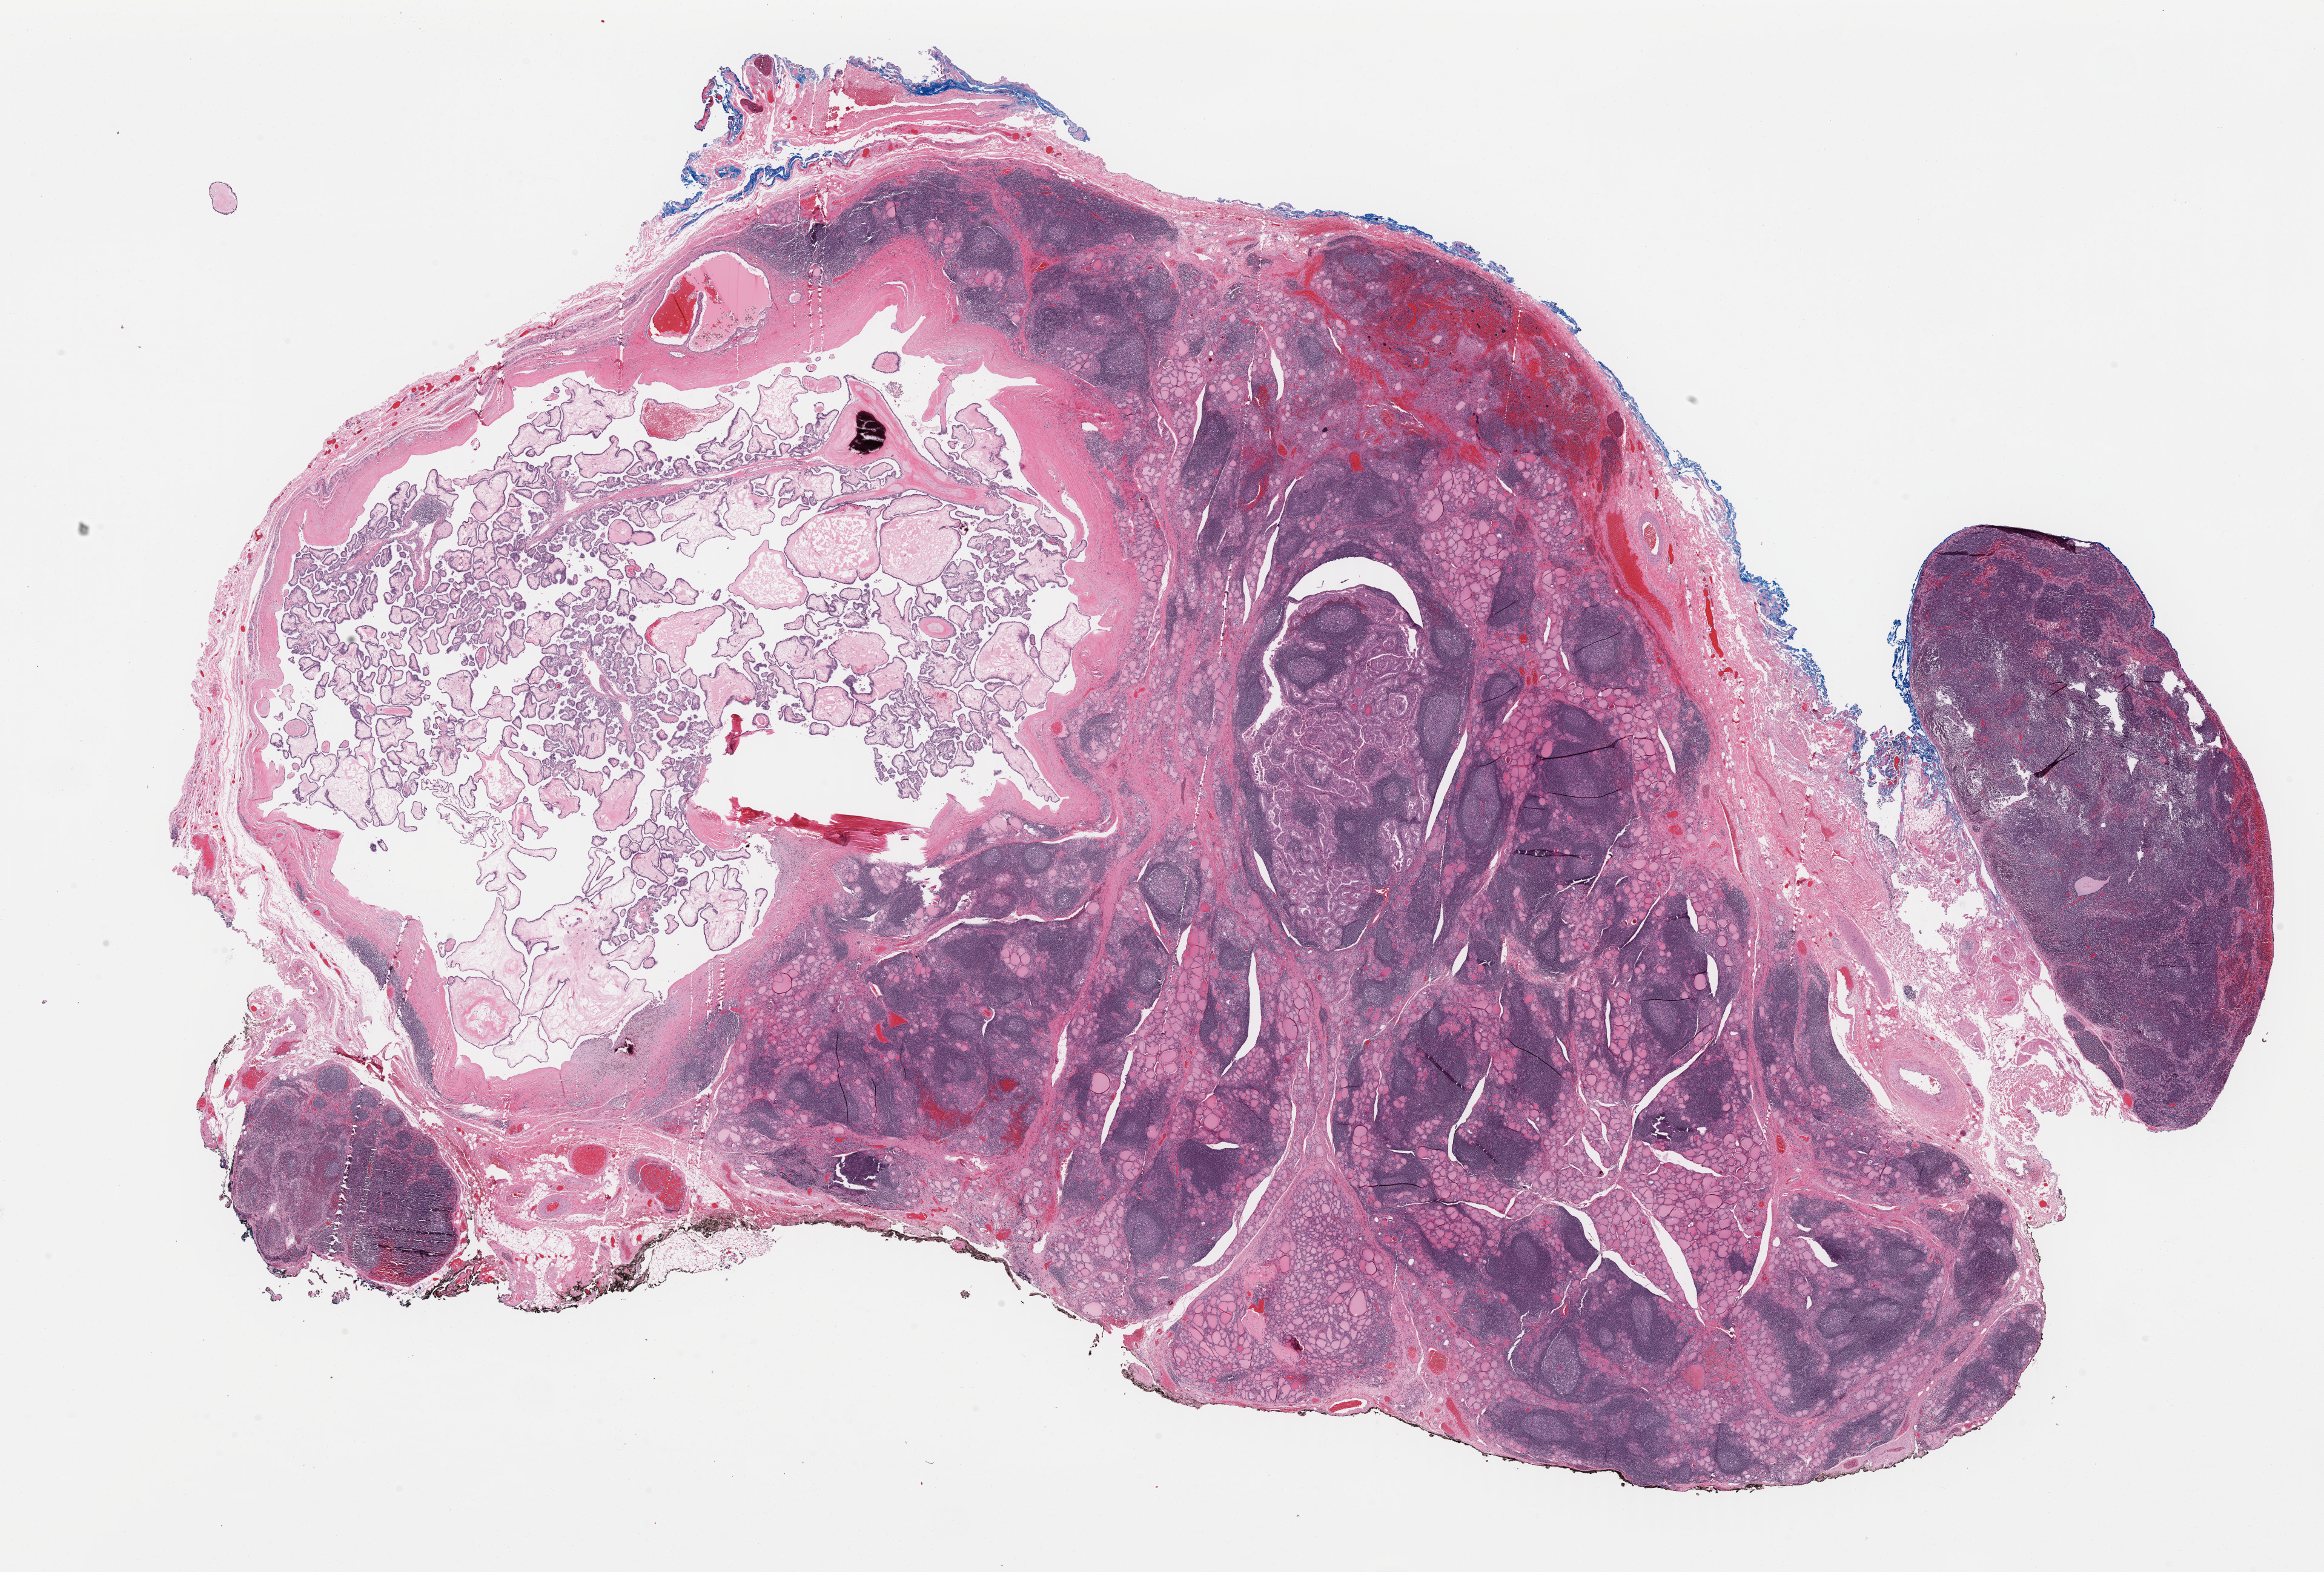
Whole-slide histology image, Hematoxylin and eosin (H&E) stained — low-resolution overview of the scanned area, about 30.3 x 20.5 mm (acquisition: 40x scan), formalin-fixed paraffin-embedded (FFPE) diagnostic section, sample: primary tumour, thyroid. Female patient; age at initial diagnosis 39 years.
Pathologic diagnosis: Papillary adenocarcinoma, NOS (thyroid gland).